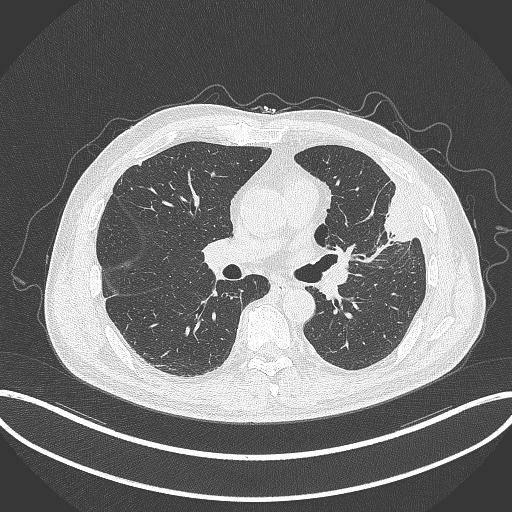
Chest CT, one axial slice. Slice 182 of 382 in the series (ordered by position). Reconstruction kernel B70f. 120 kVp. Lung window (W 1500 / L -600 HU). 1 mm slice thickness. 512 × 512 image matrix, field of view 415 × 415 mm. Patient: male, 64 years. Case-level facts recorded for this patient, not image findings: clinical TNM (as recorded): T4 N1 M0; histopathological grade: G3.
Annotated regions visible in this slice (bounding box drawn by a radiologist):
- lung tumour (recorded histology: adenocarcinoma): bounding box [x1, y1, x2, y2] px = [380, 189, 420, 245]